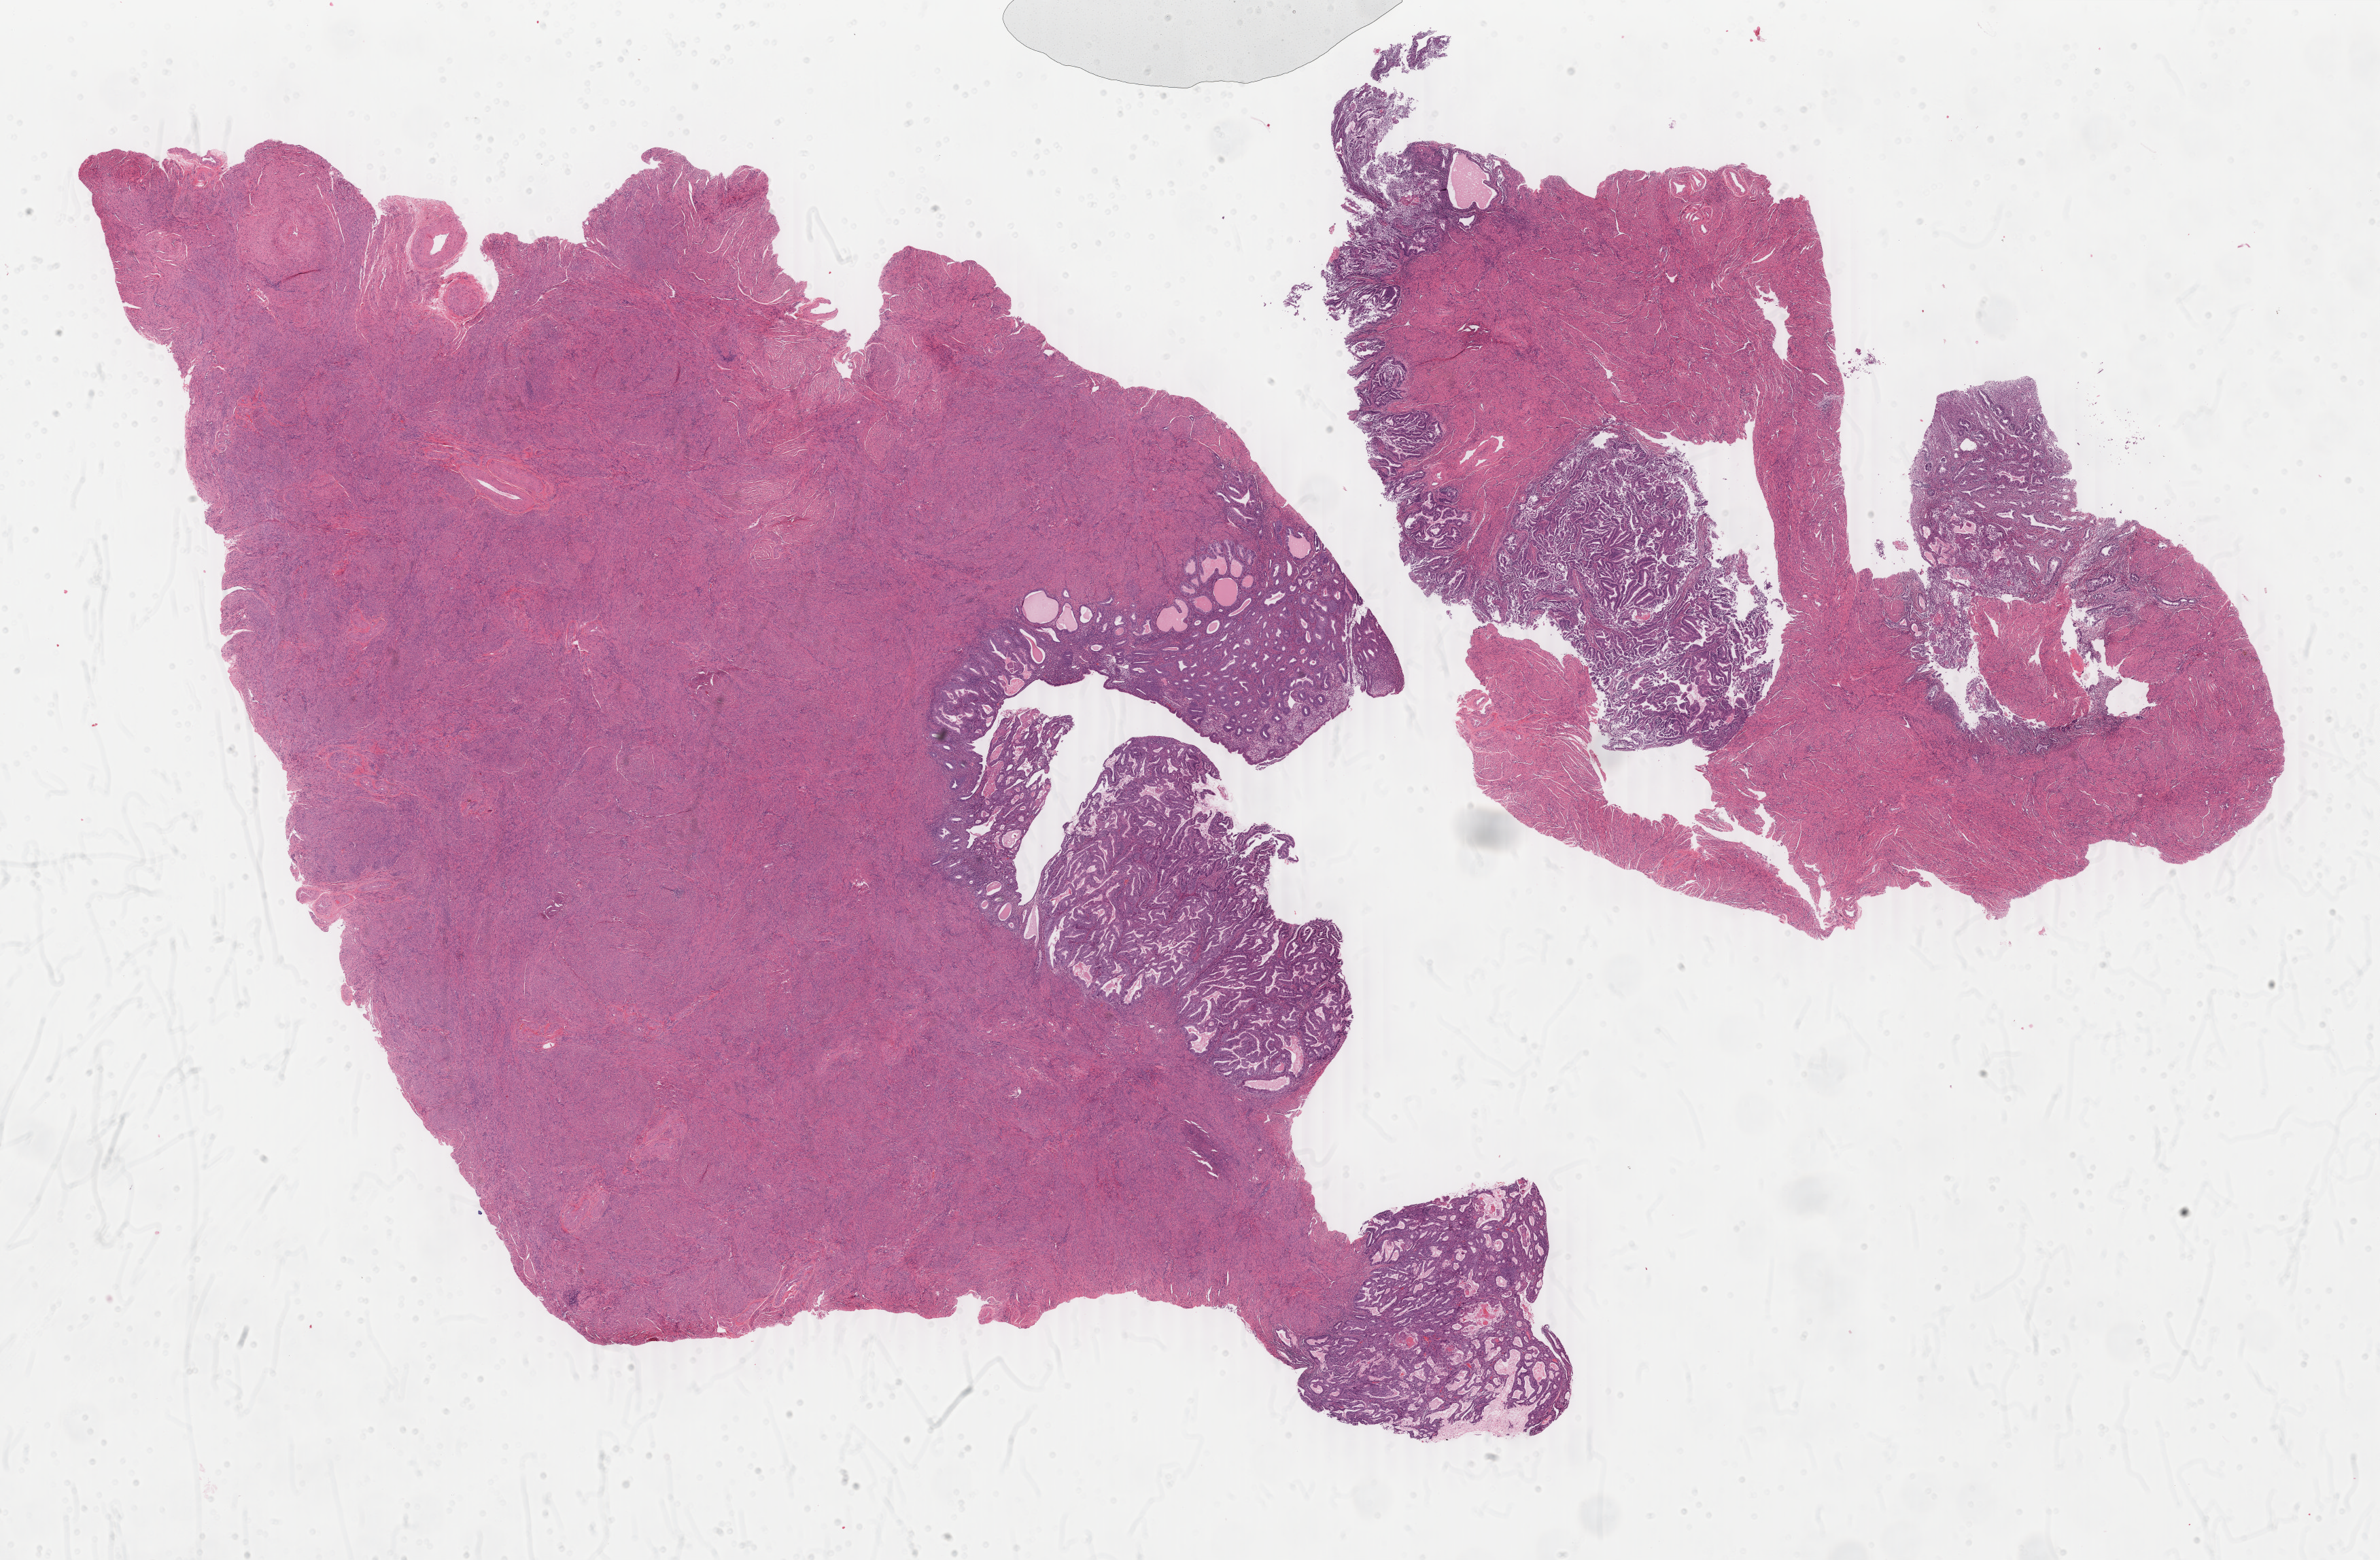
H&E whole-slide image, shown as a low-resolution overview of the whole scanned area (about 27.8 x 18.3 mm, slide scanned at 40x); FFPE section; primary tumour sample from the uterus. Female, age 60 years at initial diagnosis. Histologic grade: G1 (well differentiated).
* FIGO stage: IA
* histologic diagnosis: Endometrioid adenocarcinoma, NOS (endometrium)